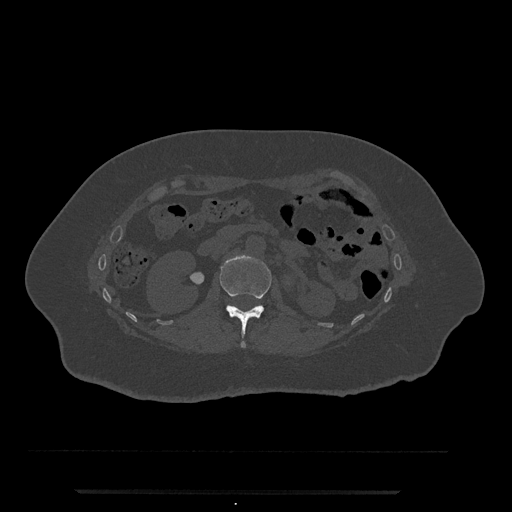
CT including the spine, one axial slice; position 96 of 797 along the scan axis; reconstruction kernel Br40s/3; bone window (W 1800 / L 400 HU); 0.5 mm slice thickness; 512 × 512 image matrix, field of view 440 × 440 mm. Patient: female, 51 years. From the clinical record (not read from this slice): primary cancer: neuro; vertebrae with lytic lesions (as recorded): T8.
Outlined on this slice (semi-automatic segmentation, software-assisted and operator-edited):
- L1 vertebra: bounding box (x1, y1, x2, y2) in pixels: (219, 255, 271, 348)